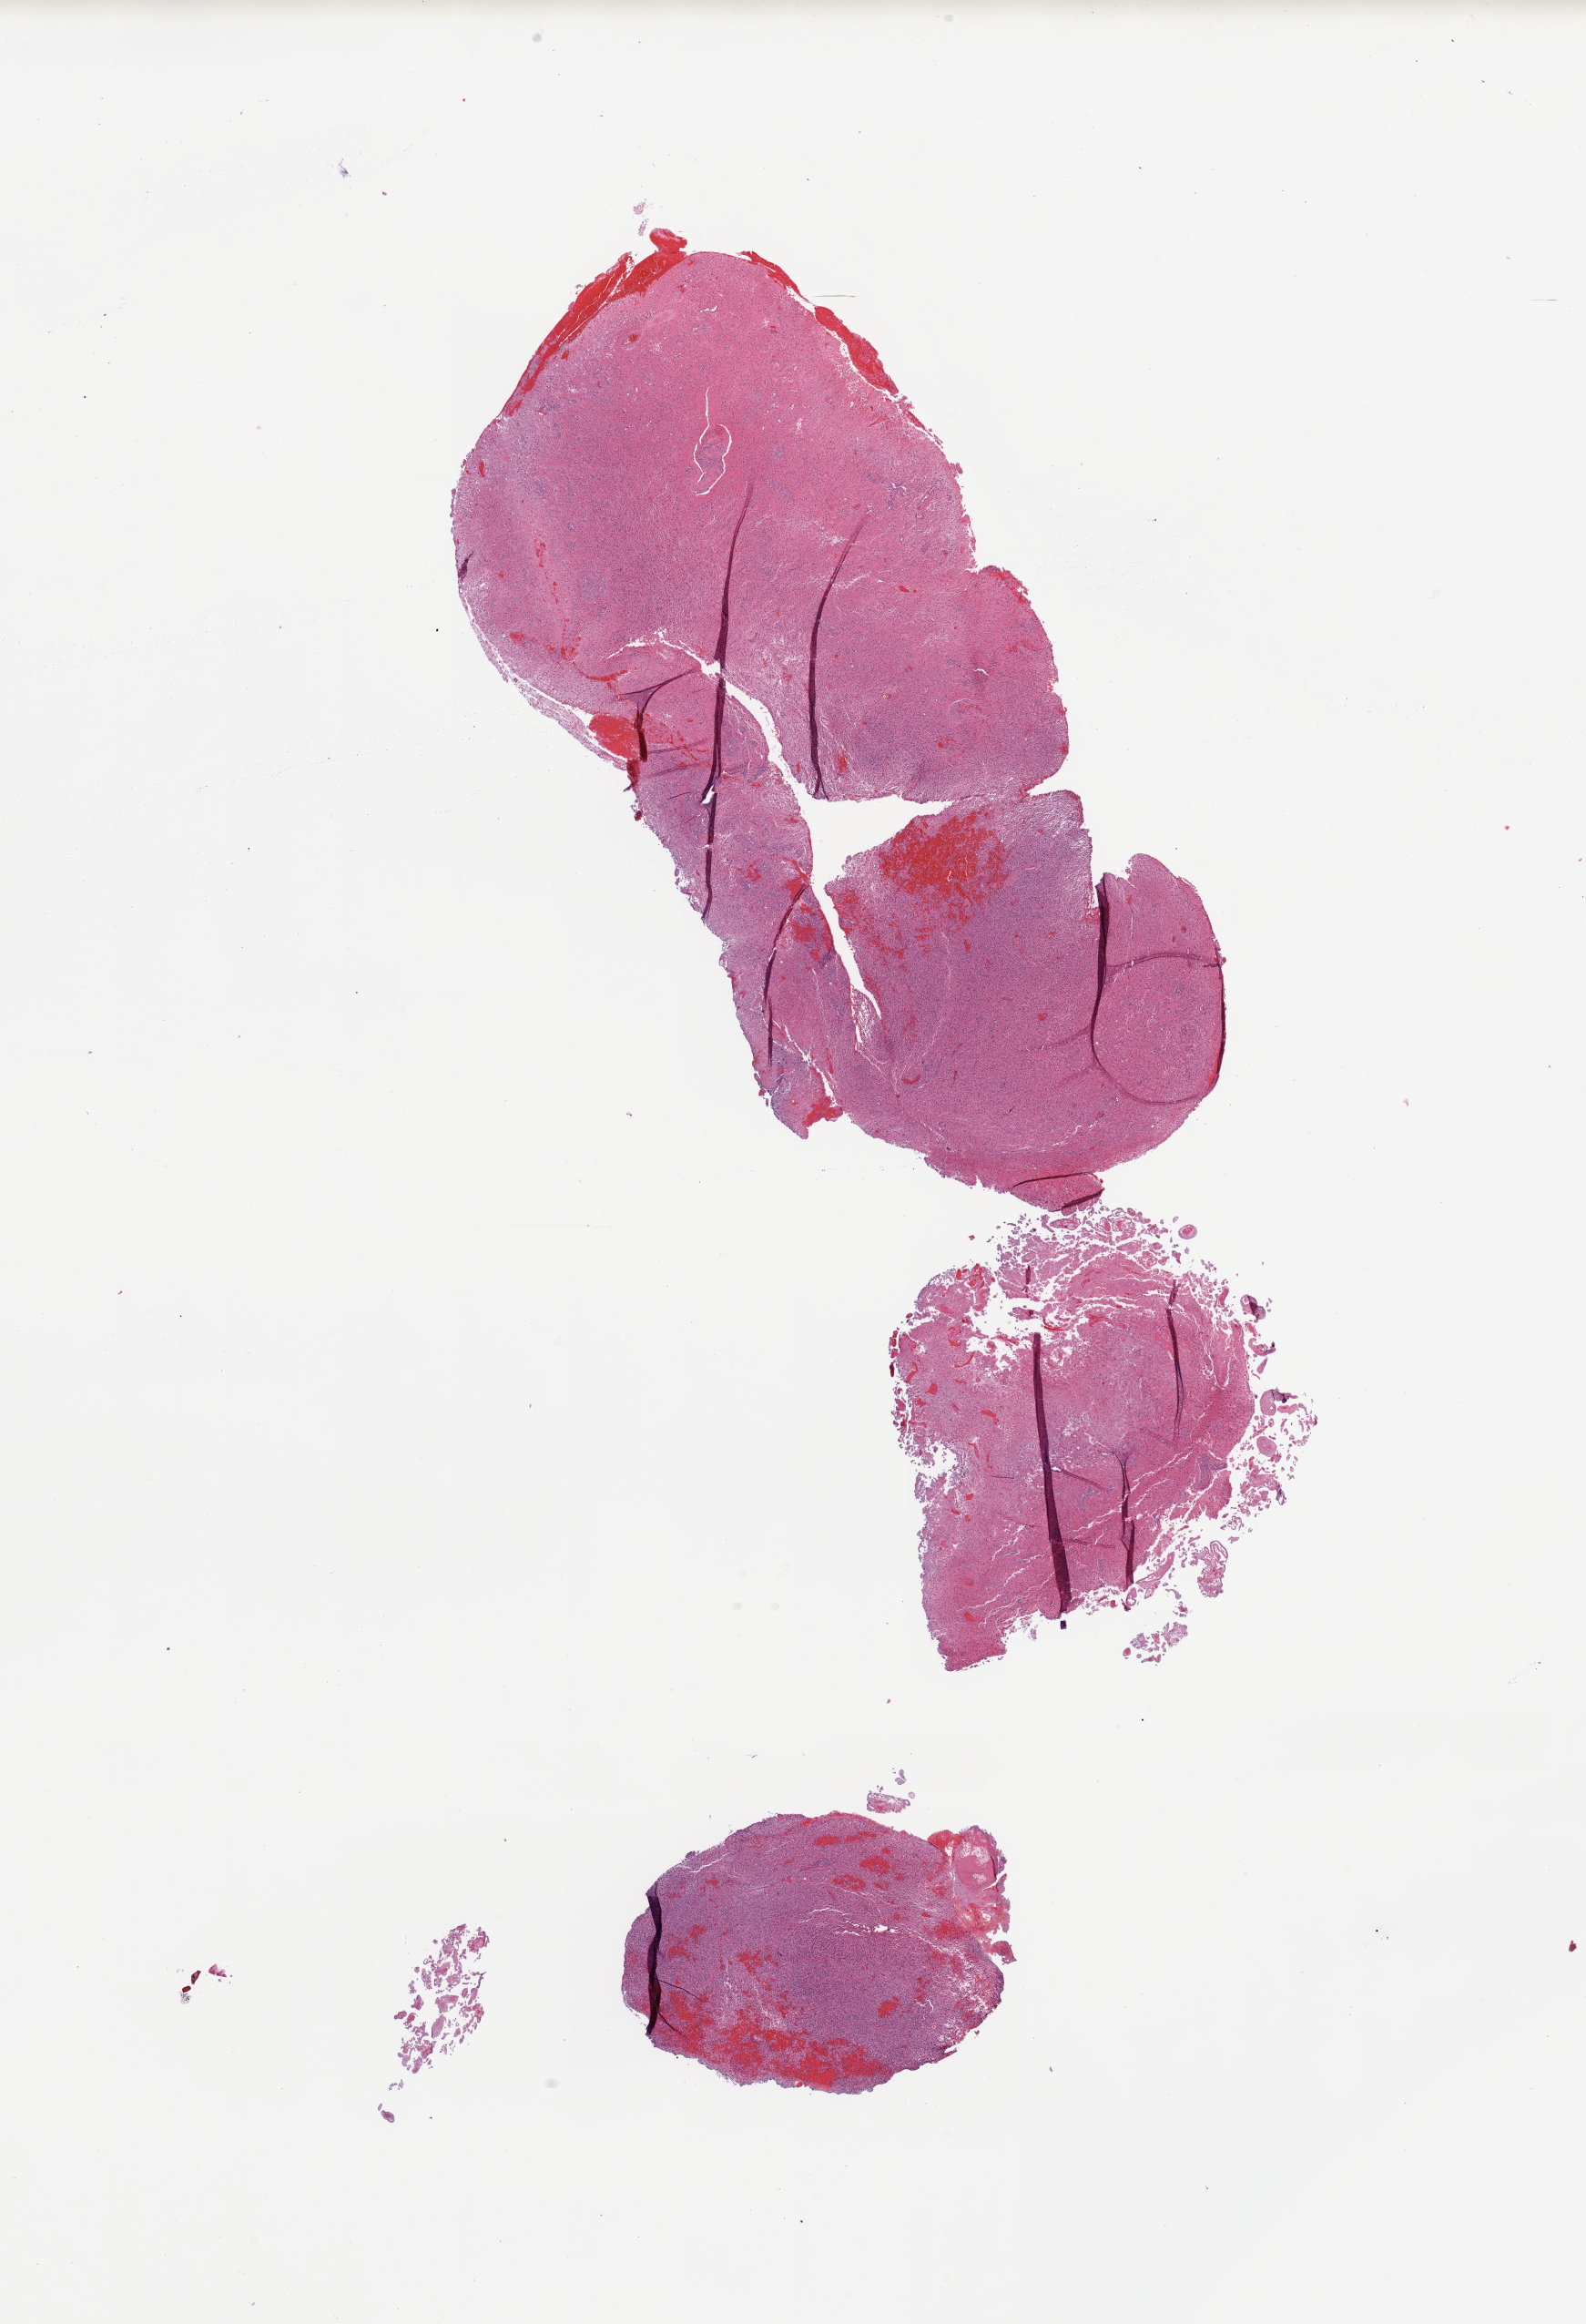
Whole-slide histology image, H&E, whole scanned area (about 13.8 x 20.2 mm) shown as a low-resolution overview; brain, tumour tissue. Patient: male, age 54 years.
• histologic diagnosis: Glioblastoma
• primary tumour site (as recorded): frontal lobe